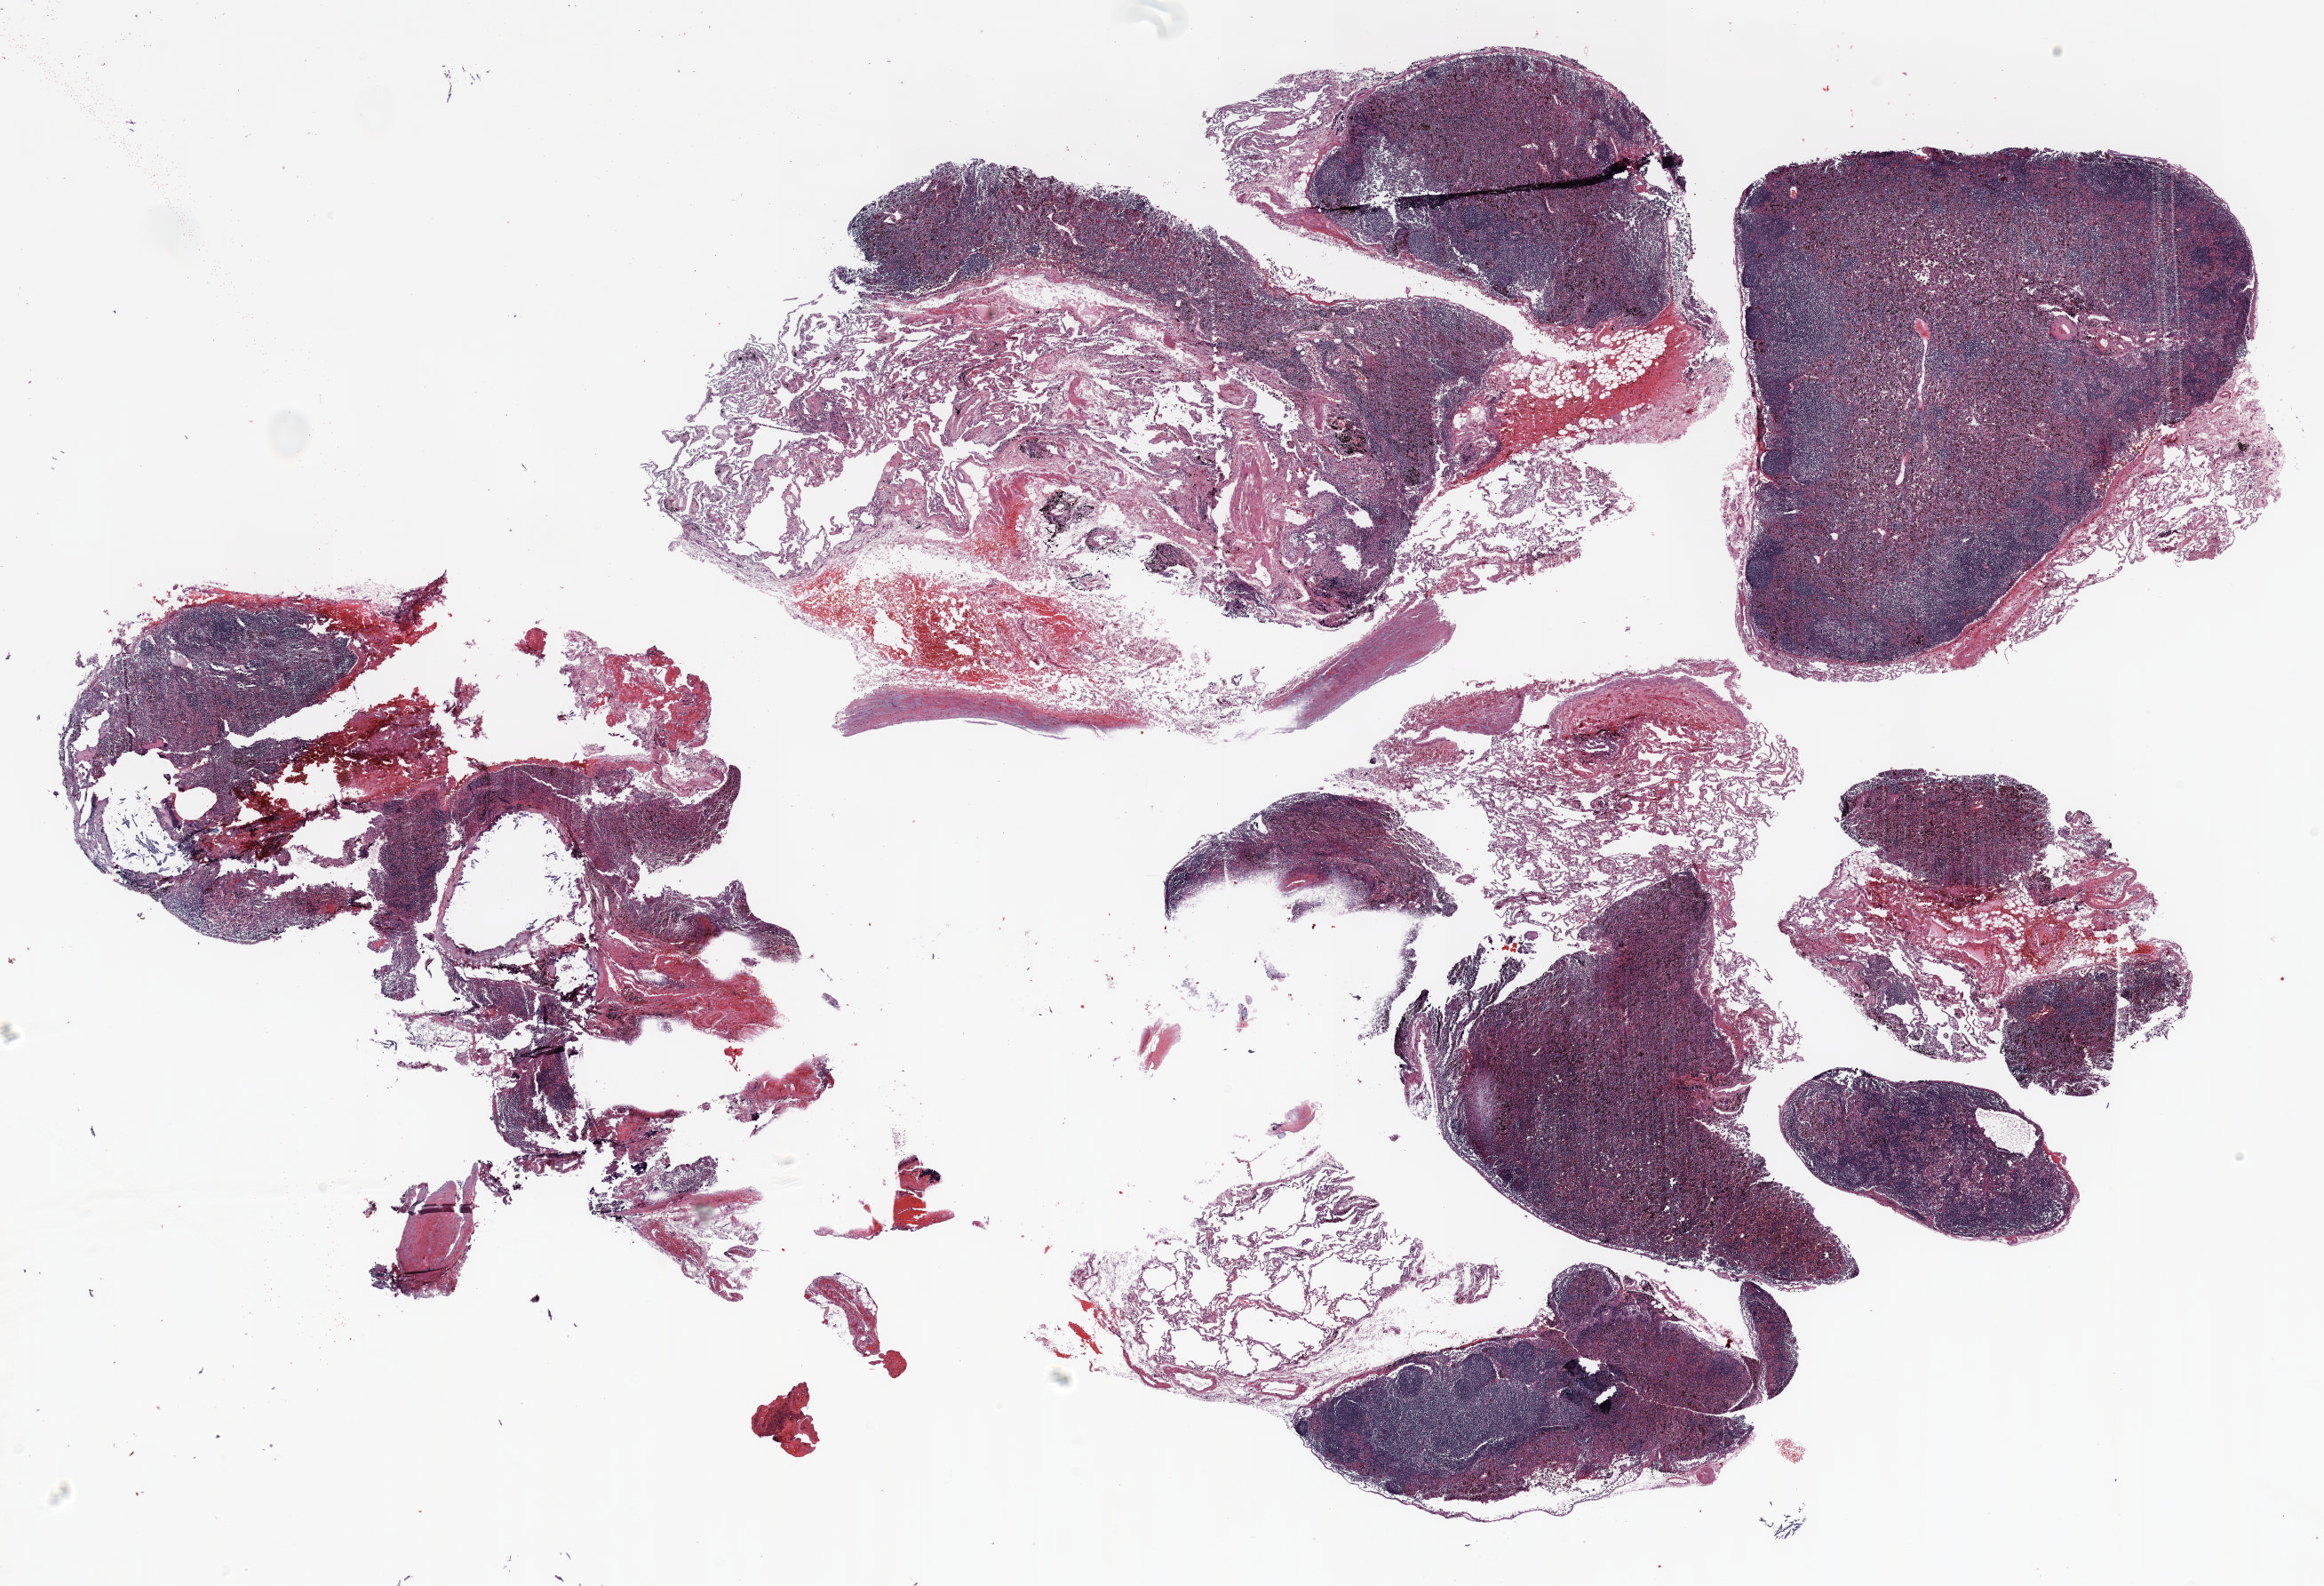
Whole-slide histology image, H&E, a low-resolution overview of the entire scanned area, about 21.0 x 14.3 mm (slide scanned at 20x). Formalin-fixed paraffin-embedded (FFPE) section. Lung tissue. Female patient, aged 59 at enrolment. Grade: moderately differentiated (G2).
Stage (AJCC 6th edition): IIB. Primary tumour location (clinical record): right lower lobe. Tumour size (pathology): 22 mm. Participant's lung-cancer diagnosis: Adenocarcinoma, NOS (ICD-O-3 8140/3).